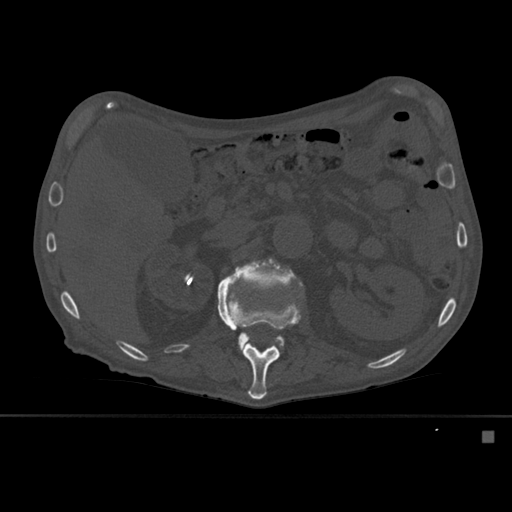
CT including the spine, one axial slice. Position 249 of 527 along the scan axis. Bone window (W 1800 / L 400 HU). 1.5 mm slice thickness. 512 × 512 image matrix, field of view 373 × 373 mm. Male patient, age 78 years. Case-level facts recorded for this patient, not image findings: primary cancer: prostate.
Annotated regions visible in this slice (semi-automatic segmentation, software-assisted and operator-edited):
- L1 vertebra: box from (x=217, y=278) to (x=301, y=400) px
- L2 vertebra: (x=227, y=257)–(x=303, y=348)